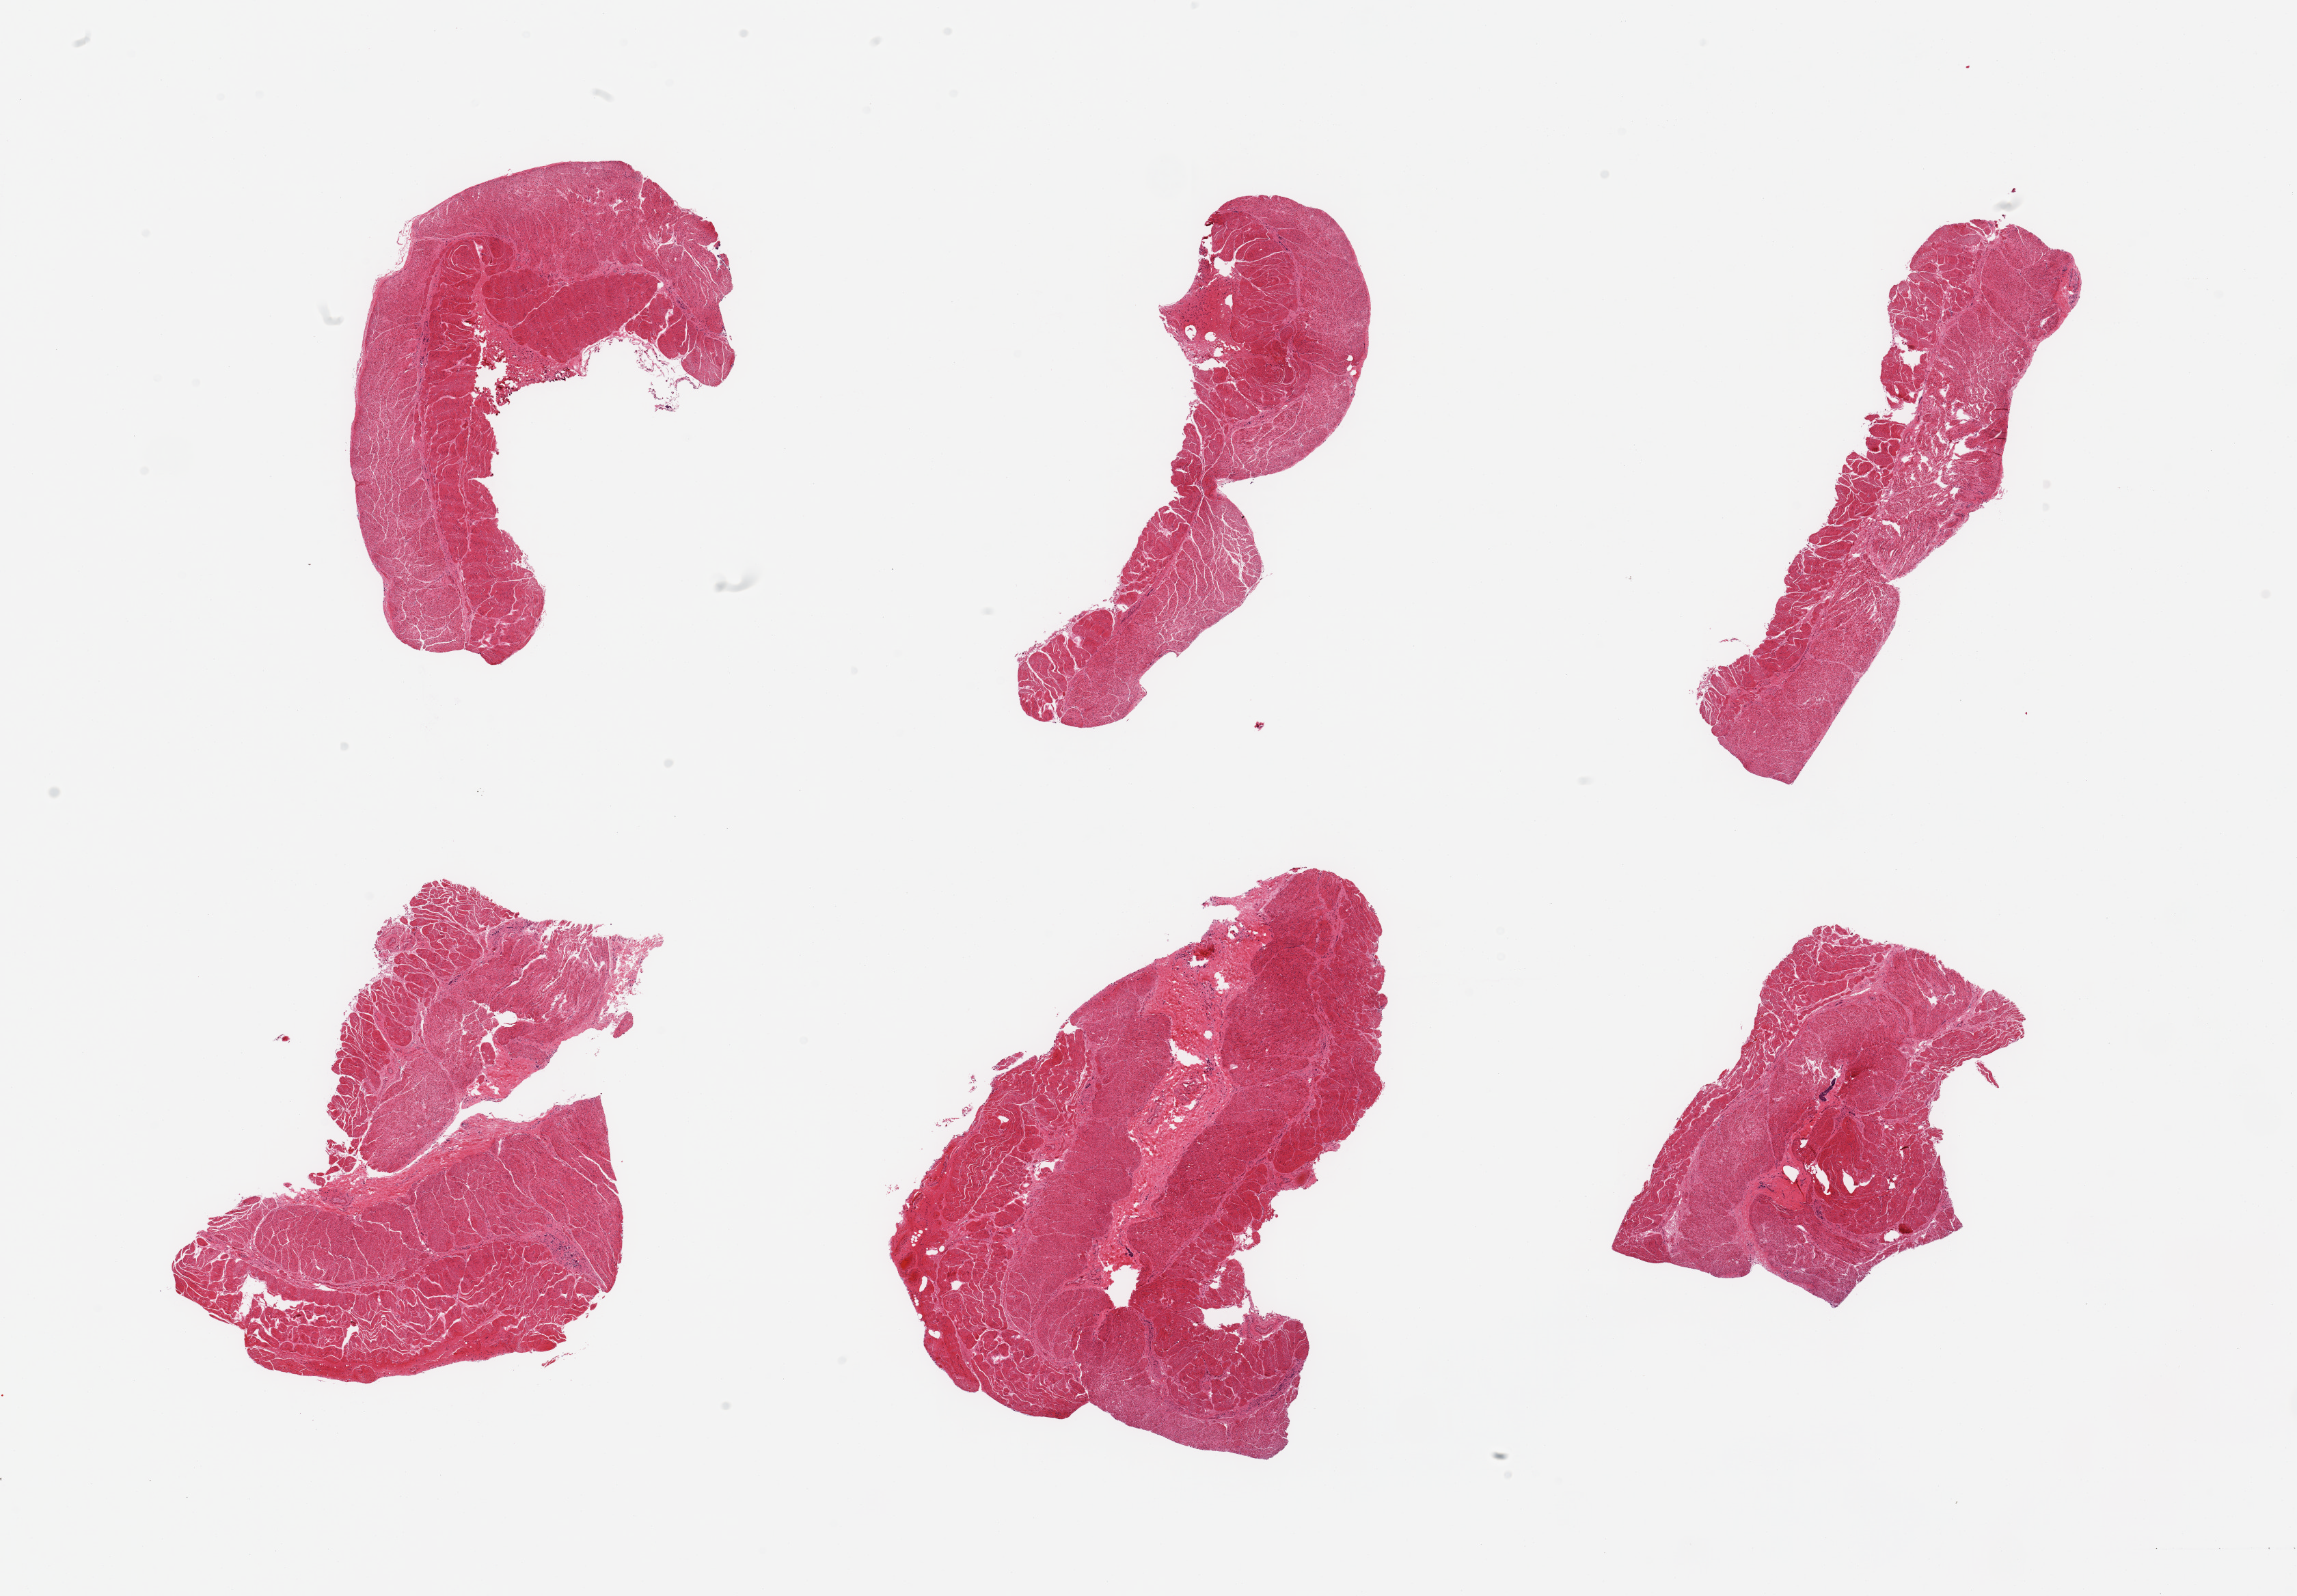
H&E whole-slide image — low-resolution overview of the scanned area, about 26.6 x 18.5 mm; PAXgene-fixed, paraffin-embedded tissue; sampled site (target tissue): esophageal muscle; donor tissue sample. Donor: female.
Review note (as recorded): 6 pieces; target muscularis.